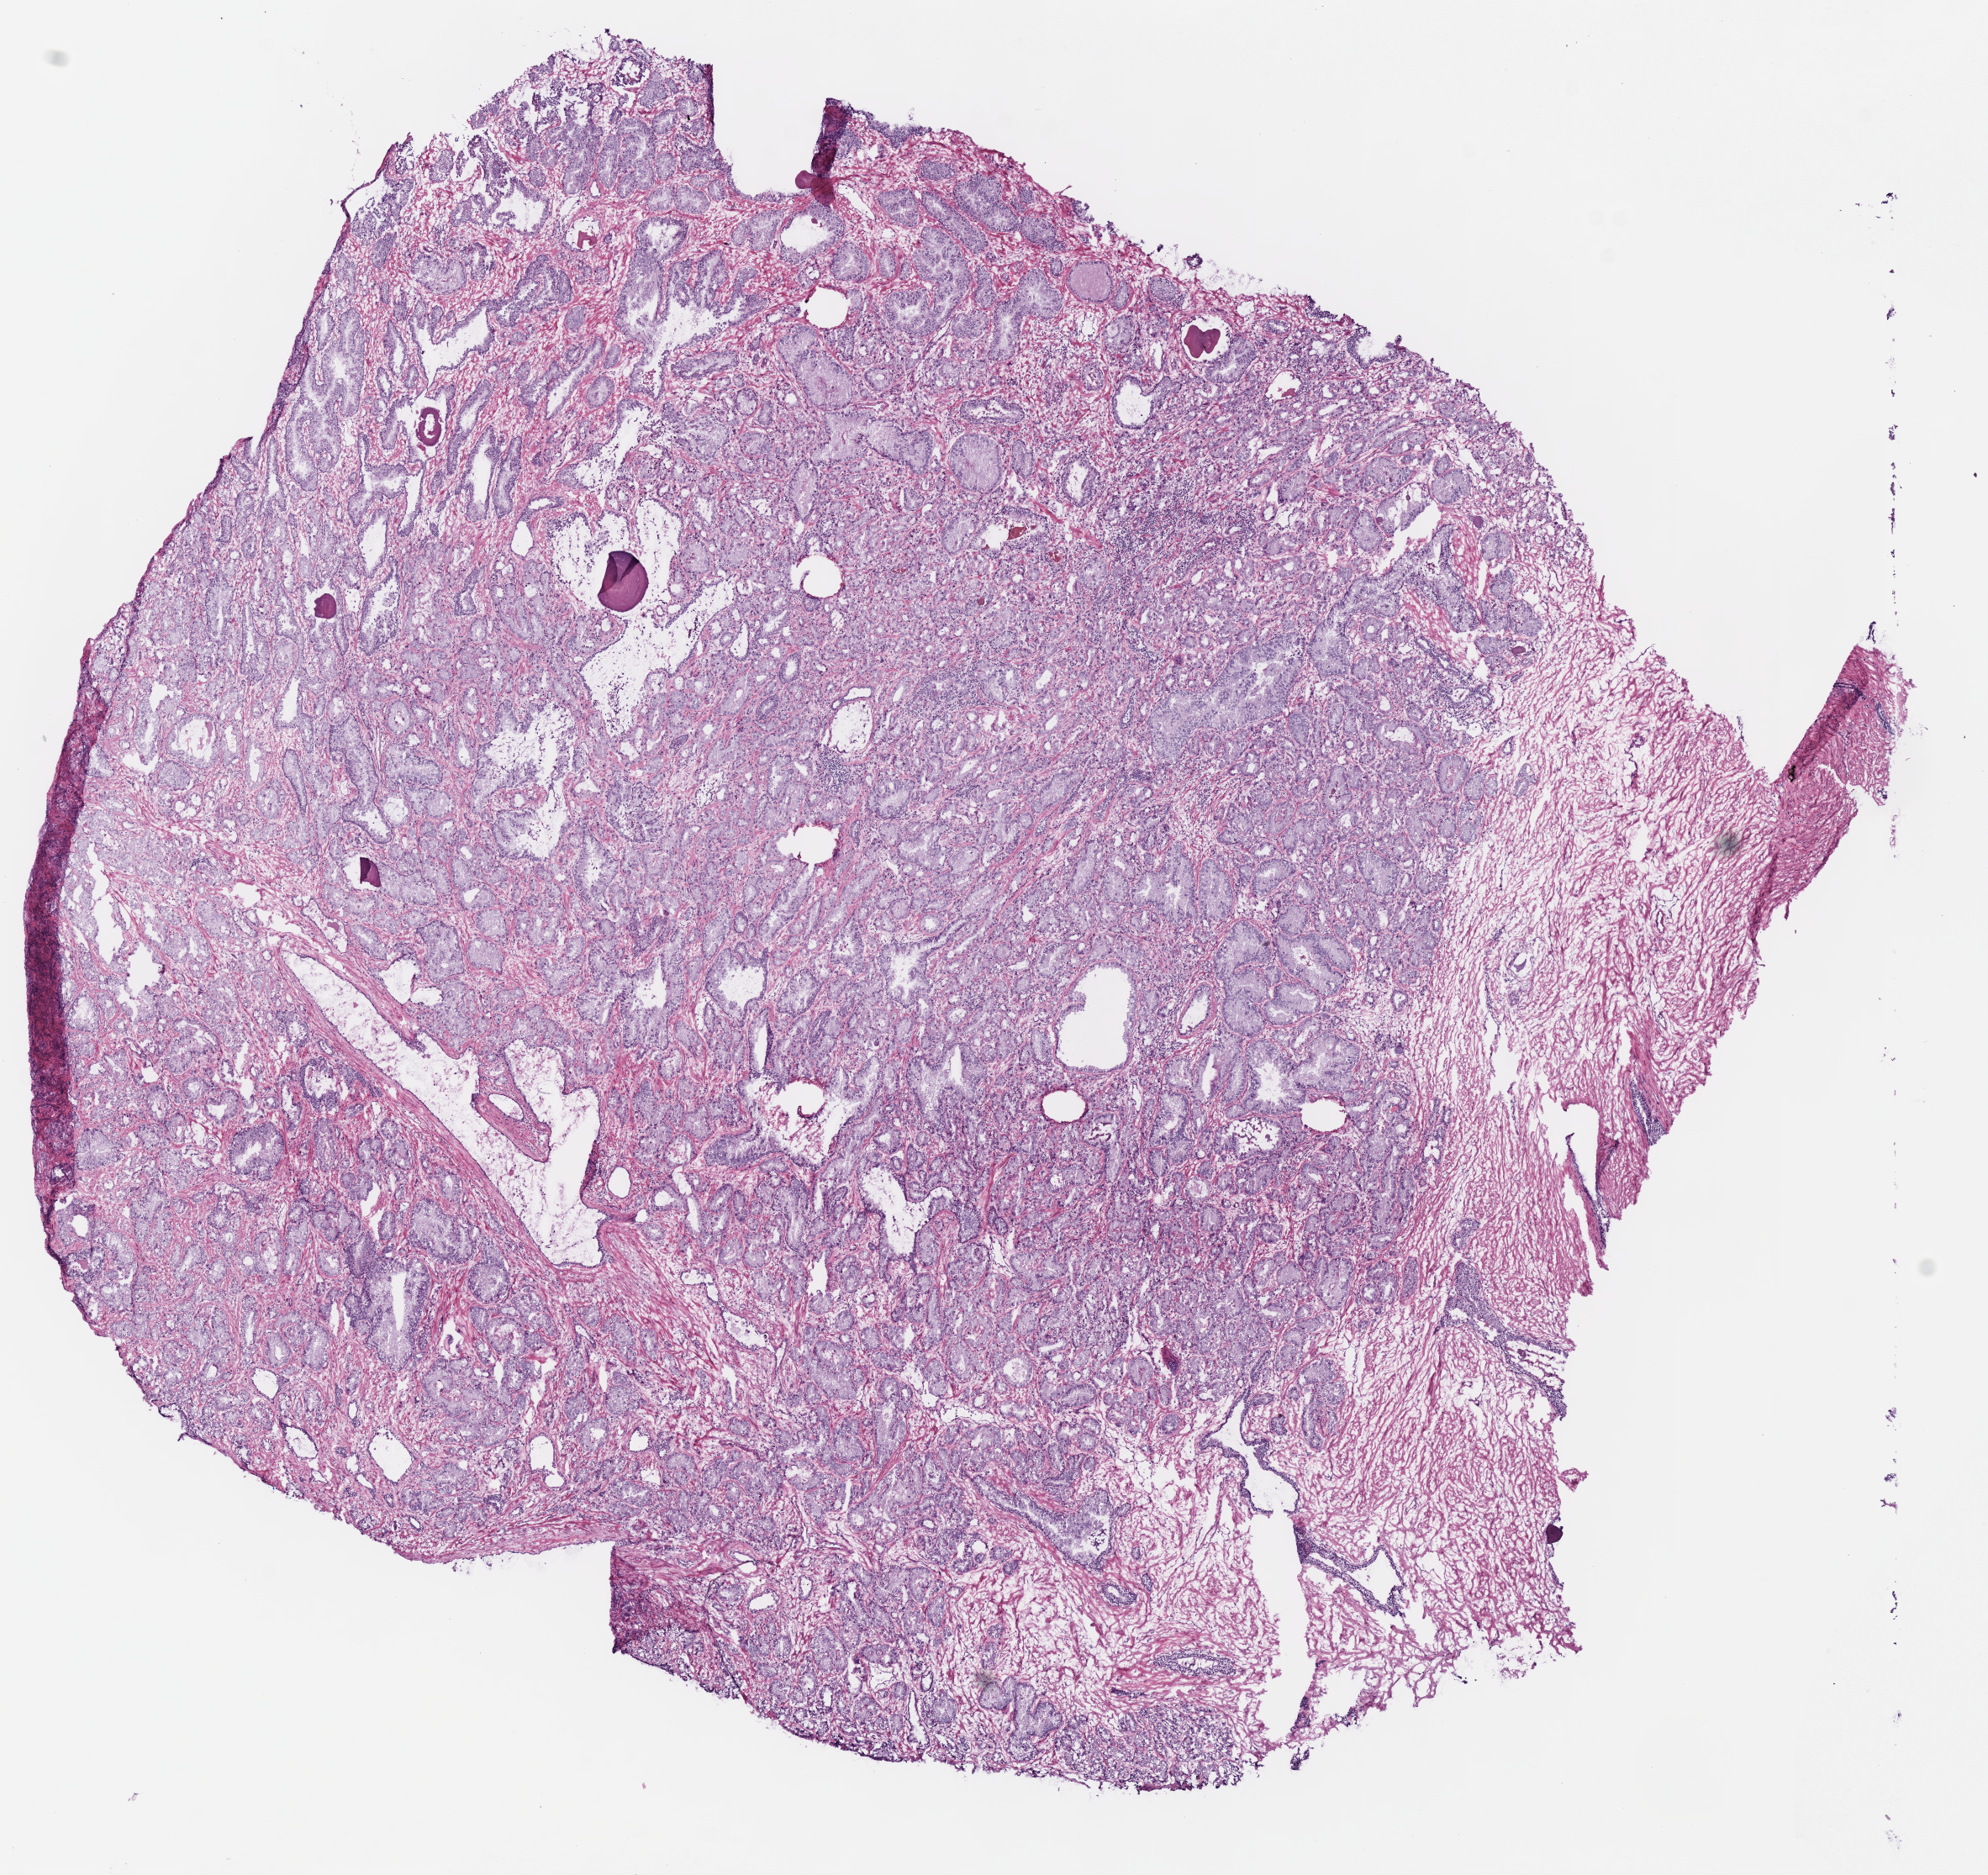
H&E-stained whole-slide image, low-resolution overview of the scanned area, about 9.3 x 8.8 mm (from a 40x scan). Frozen section from the bottom of the tissue portion. Sample: primary tumour, prostate. Male, age 59 years at initial diagnosis. Gleason score: 7 (3+4).
* diagnosis: Acinar cell carcinoma (prostate gland)
* lymph nodes positive (case pathology): 0 of 13 examined